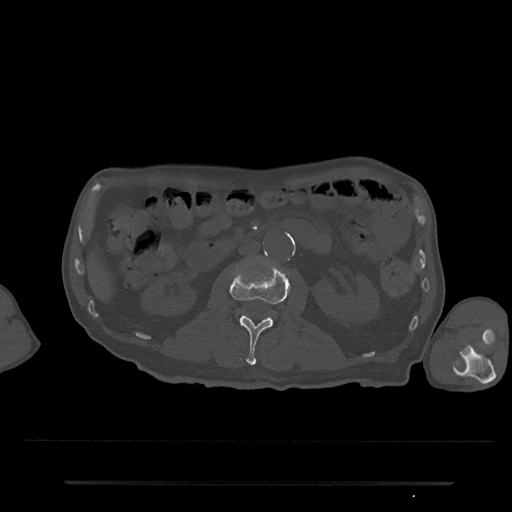
CT including the spine, one axial slice. Slice 41 of 797 in the series (ordered by position). Reconstruction kernel Br40s/3. 120 kVp. Bone window (W 1800 / L 400 HU). 512 × 512 image matrix, field of view 427 × 427 mm. Male patient, age 74 years. From the clinical record (not read from this slice): primary cancer: prostate.
Structures marked on this image (semi-automatic segmentation, software-assisted and operator-edited):
- L2 vertebra: bounding box (x1, y1, x2, y2) in pixels: (229, 259, 291, 366)